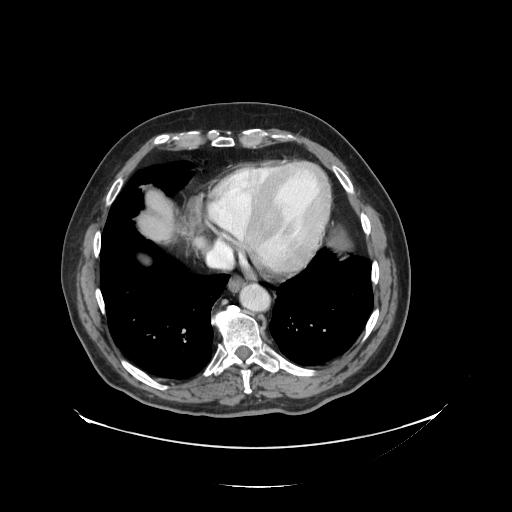
Contrast-enhanced abdominal CT, one axial slice. Position 124 of 138 along the scan axis. Intravenous contrast given. Soft-tissue window (W 400 / L 40 HU). 2.5 mm slice thickness. 512 × 512 image matrix, field of view 497 × 497 mm. Male patient, age 77 years. Case-level facts recorded for this patient, not image findings: diagnosis: colorectal cancer liver metastases, imaged before liver resection; multiple liver metastases: no.
Outlined on this slice (expert manual segmentation):
- liver: bounding box [x1, y1, x2, y2] px = [139, 191, 174, 241]
- planned liver remnant (the part of the liver to remain after resection): [138, 191, 174, 240]